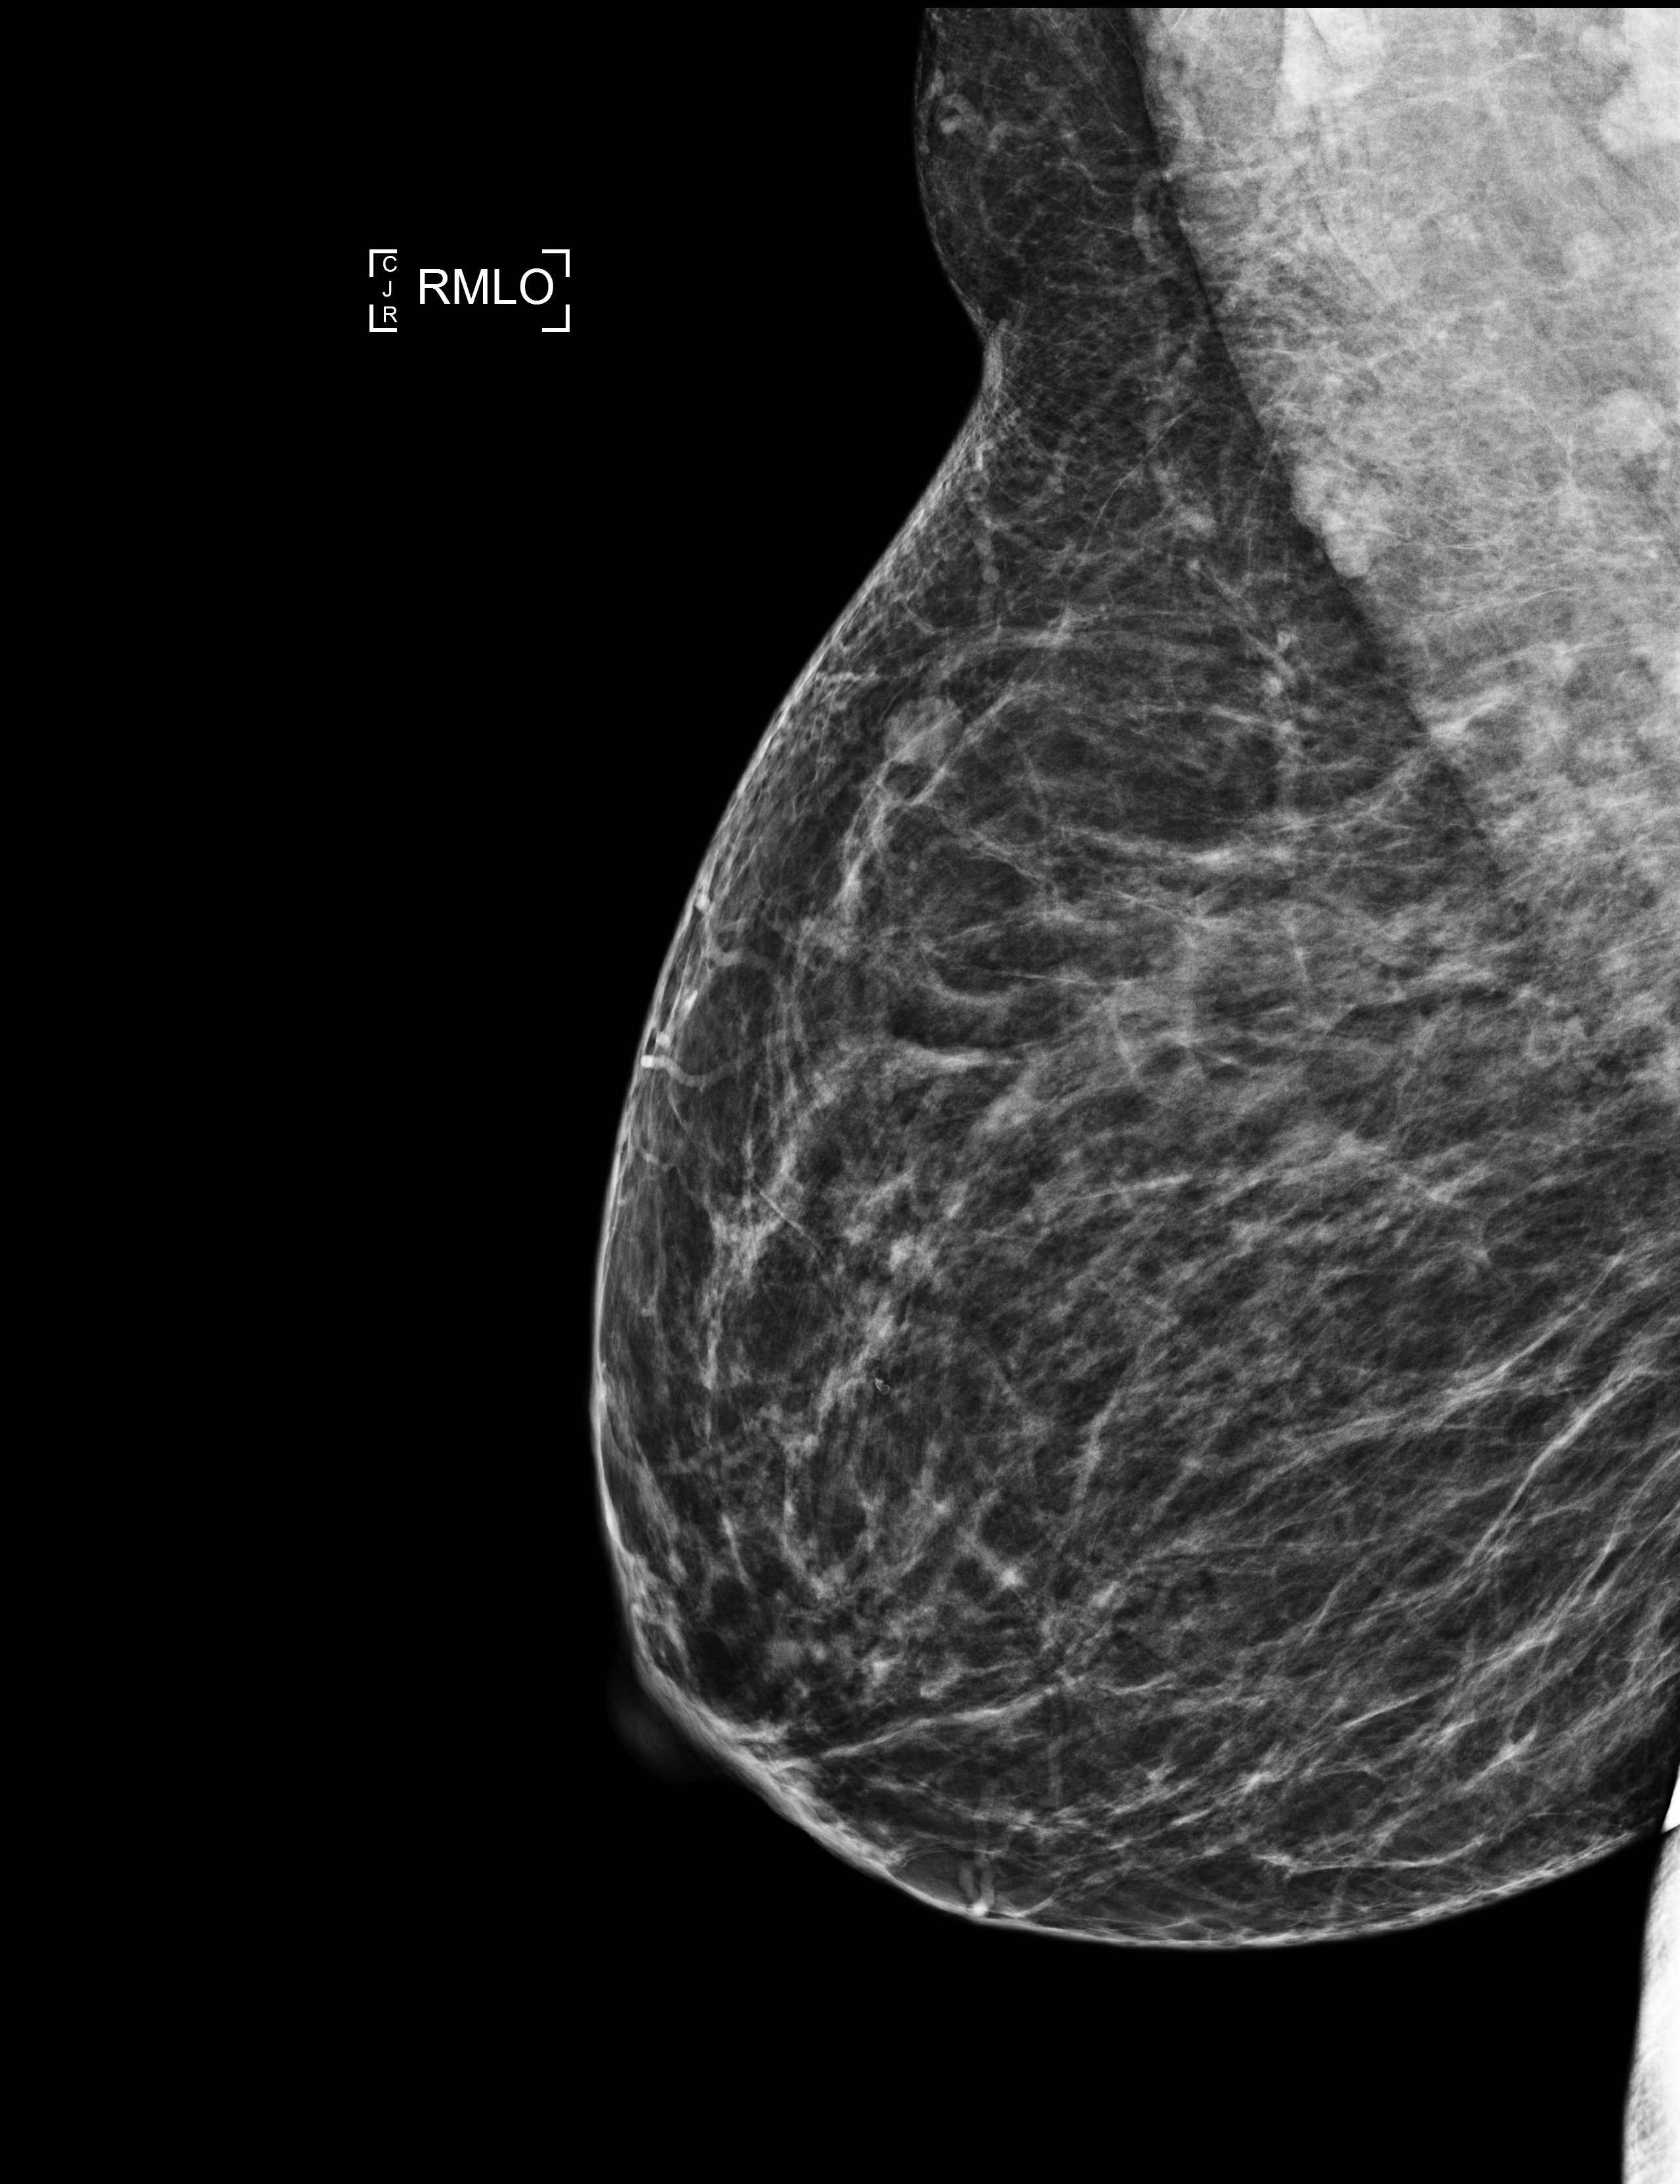
Screening examination; compressed breast thickness 72 mm; system: Selenia Dimensions. Patient: female, 44 years.
Image type: full-field digital mammogram. Breast: right. Projection: medio-lateral oblique projection.